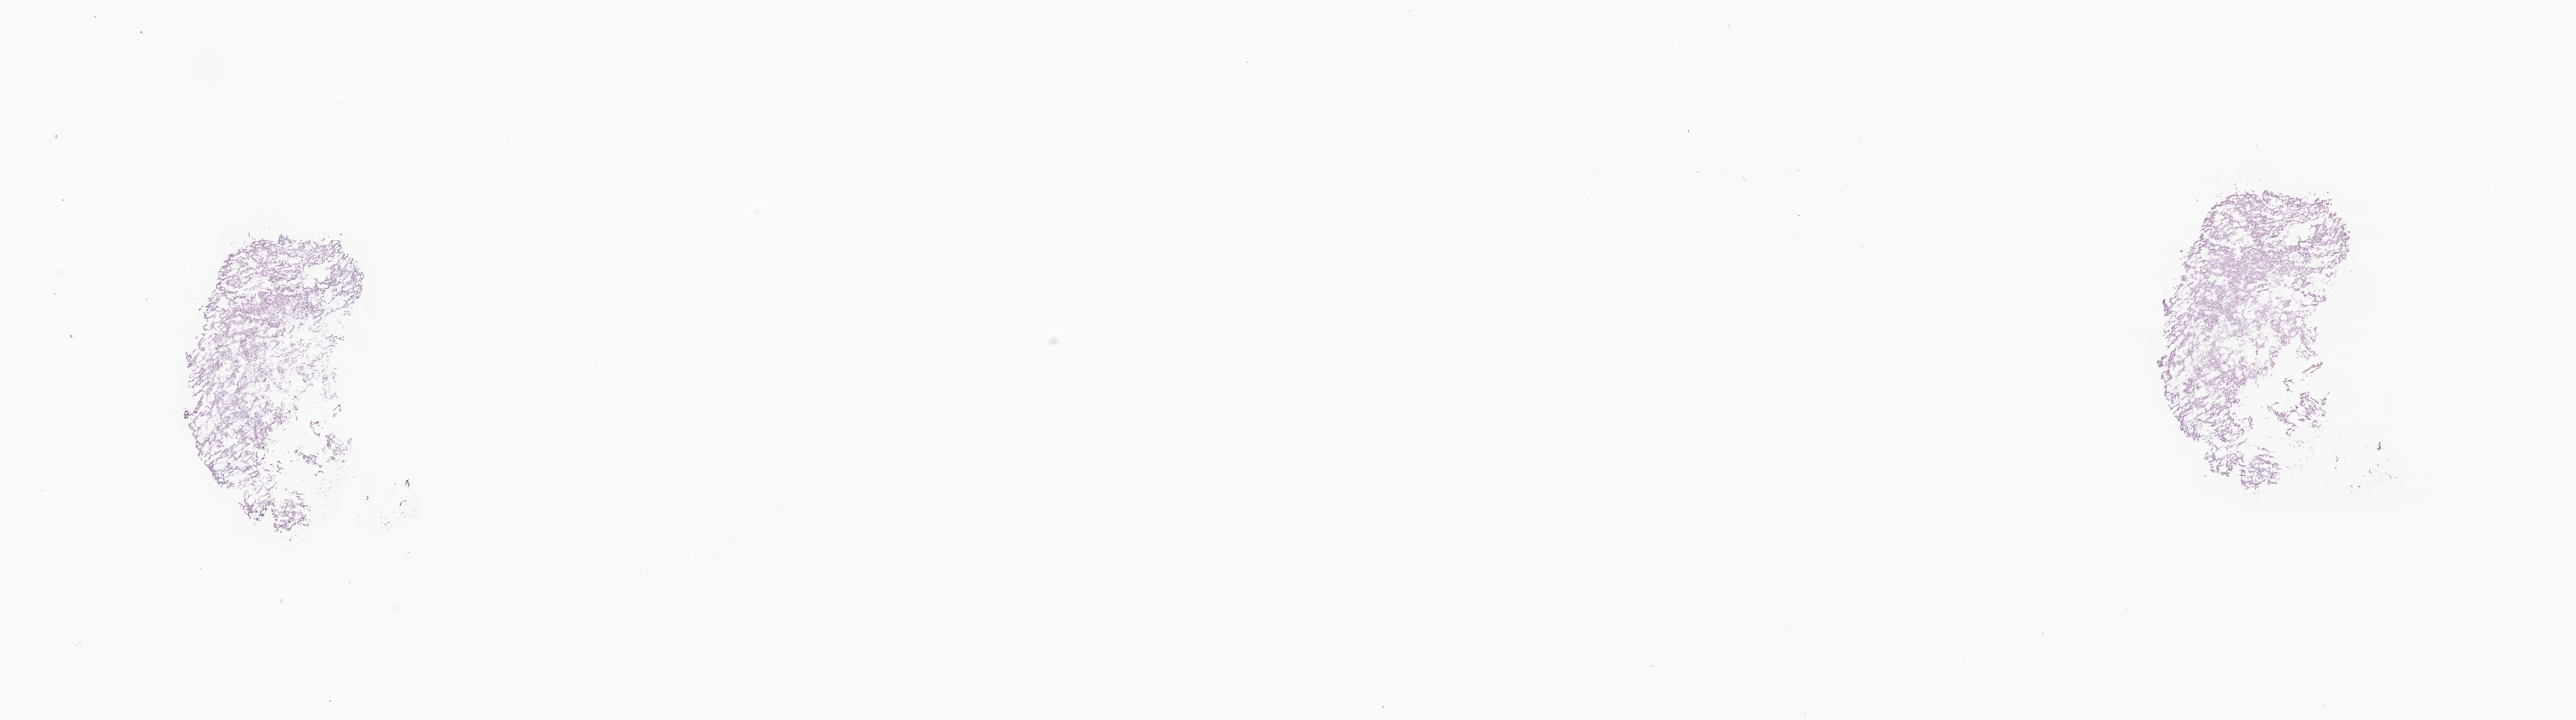
H&E whole-slide image of tumor tissue from the brain — a low-resolution overview of the entire scanned area, about 27.7 x 7.7 mm; frozen section. Male patient, age 74 months (6 years 2 months).
• diagnosis (ICD-O-3 morphology term): Dysembryoplastic neuroepithelial tumor